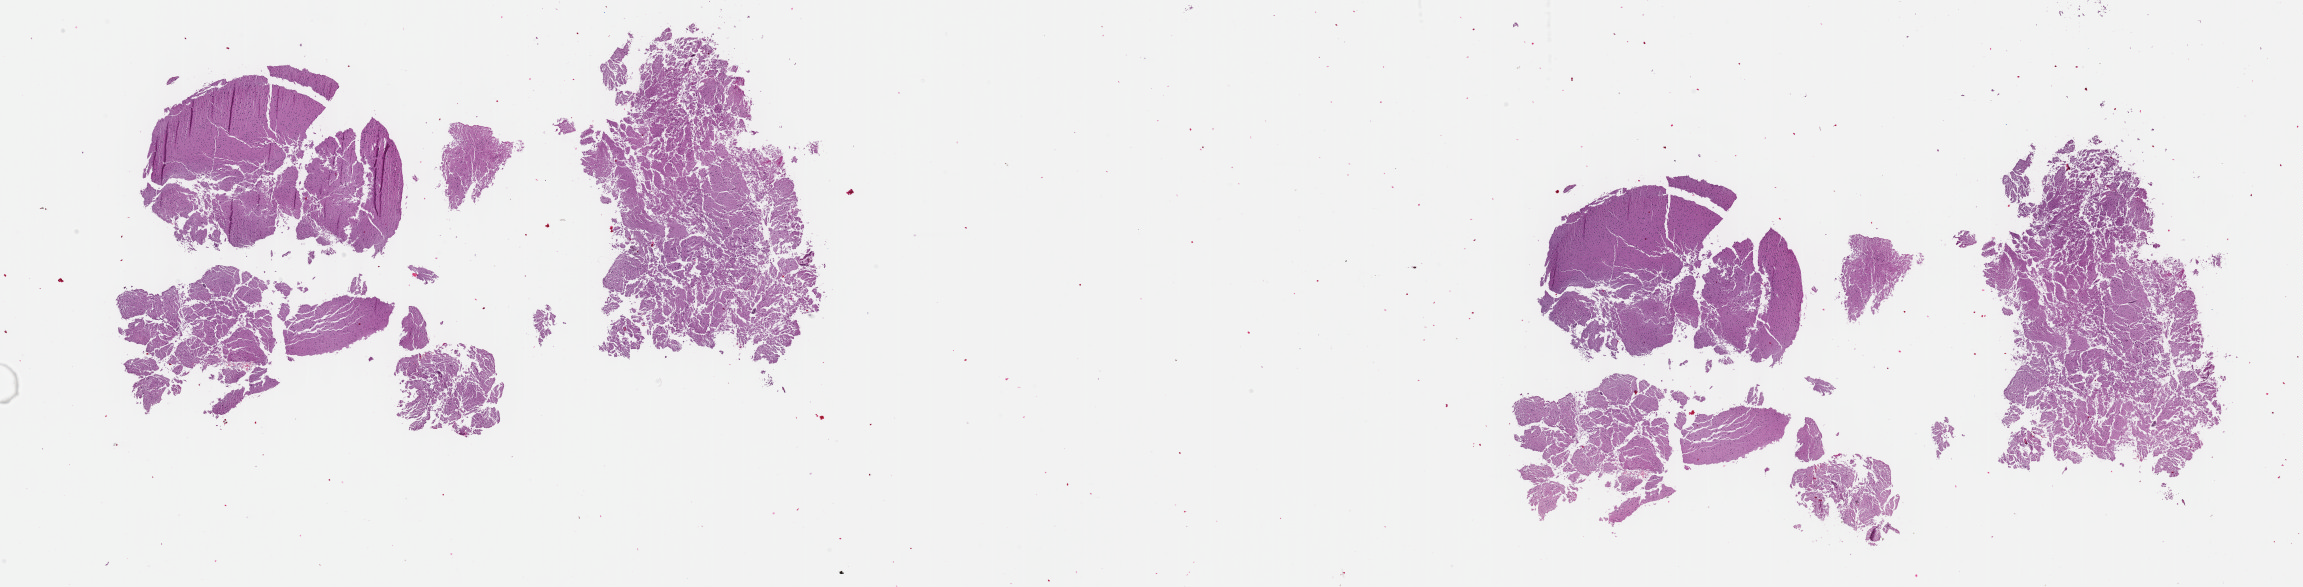
Digitized Hematoxylin and eosin (H&E) stained tissue section (whole slide) — whole scanned area (about 37.2 x 9.5 mm, slide scanned at 40x) shown as a low-resolution overview. FFPE section. Brain, primary tumour sample. Female, age 74 years at initial diagnosis. Histologic grade: G2 (moderately differentiated).
• pathologic diagnosis: Mixed glioma